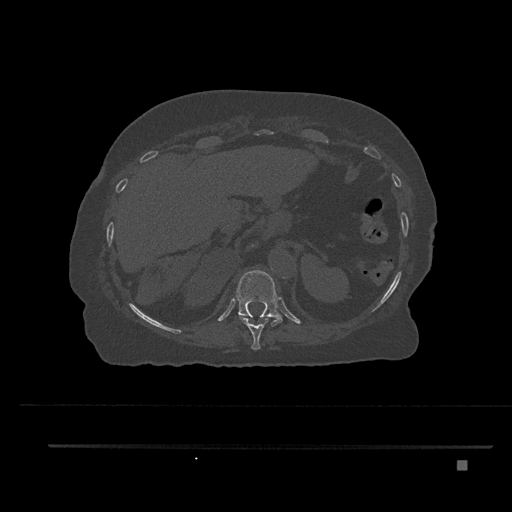
CT including the spine, one axial slice; position 328 of 797 along the scan axis; reconstruction kernel Br40s/3; 120 kVp; bone window (W 1800 / L 400 HU); 0.5 mm slice thickness; 512 × 512 image matrix, field of view 437 × 437 mm. Patient: female, 76 years. From the clinical record (not read from this slice): primary cancer: lung; vertebrae with lytic lesions (as recorded): T11, L3.
Annotated regions visible in this slice (semi-automatically segmented with operator editing):
- T10 vertebra: bounding box [x1, y1, x2, y2] px = [239, 316, 270, 350]
- T11 vertebra: [235, 270, 282, 326]